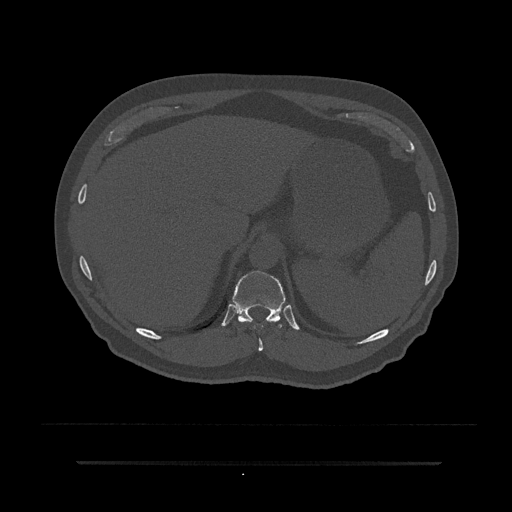
CT including the spine, one axial slice; 120 kVp; bone window (W 1800 / L 400 HU); 0.5 mm slice thickness; 512 × 512 image matrix. Male patient, age 59 years. Case-level facts recorded for this patient, not image findings: primary cancer: bile ducts.
Structures marked on this image (semi-automatic segmentation, software-assisted and operator-edited):
- T10 vertebra: bounding box (x1, y1, x2, y2) in pixels: (238, 319, 277, 352)
- T11 vertebra: (232, 271, 287, 328)